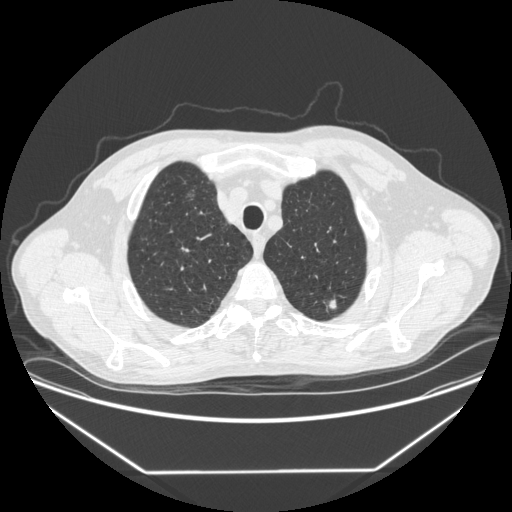
Low-dose screening chest CT, one axial slice; slice 333 of 383 in the series (ordered by position); lung window (W 1500 / L -600 HU); 1.25 mm slice thickness; 512 × 512 image matrix, field of view 418 × 418 mm.
Structures marked on this image (outlined manually by an expert reader):
- lesion 1 (tumor, upper lobe of left lung): box from (x=327, y=299) to (x=337, y=309) px